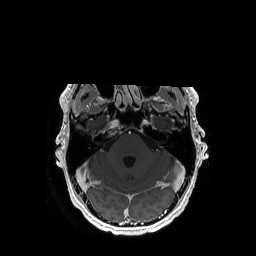
Brain MRI from a brain-tumour surgery series, one axial slice. Position 126 of 192 along the scan axis. T1-weighted post-contrast. 256 × 256 image matrix, field of view 256 × 256 mm. From the clinical record (not read from this slice): histopathology: Astrocytoma; WHO grade: 3; IDH mutation: yes; tumour location: Left Temporal.
Annotated regions visible in this slice (outlined manually by an expert reader):
- tumour: bounding box (x1, y1, x2, y2) in pixels: (158, 123, 163, 133)